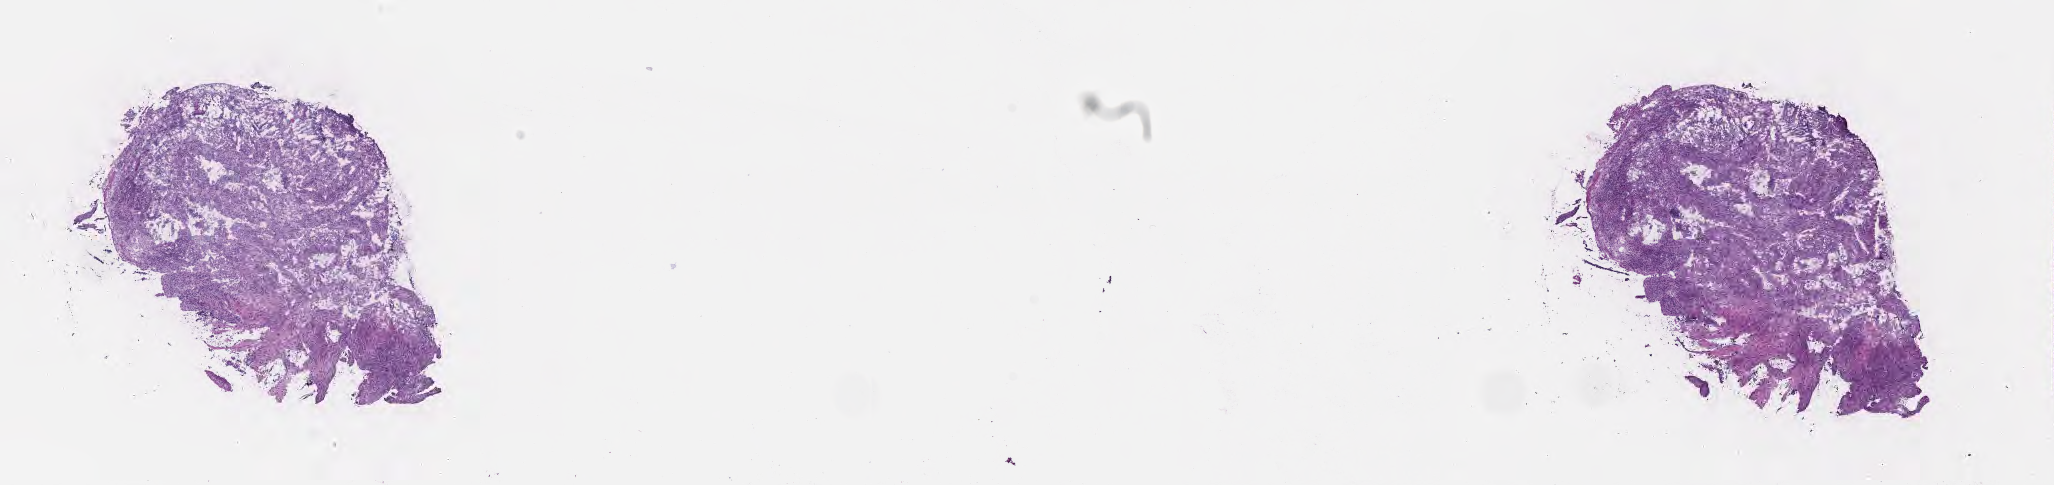
H&E whole-slide image — low-resolution overview of the scanned area, about 16.6 x 3.9 mm; frozen section (tissue freezing medium); specimen: primary tumor; site: sigmoid colon. Patient: male, age at initial diagnosis 75 years. Tumor grade: G2 (moderately differentiated). Composition of this section per pathologist review: tumor cells 75%, tumor nuclei 75%, stromal cells 25%, necrosis 0%, normal cells 0%. Inflammatory infiltration, as recorded: lymphocyte infiltration 6%, monocyte infiltration 2%, neutrophil infiltration 10%.
AJCC pathologic stage: Stage IIIA. Diagnosis: Adenocarcinoma, NOS. Section: top of the tissue portion.